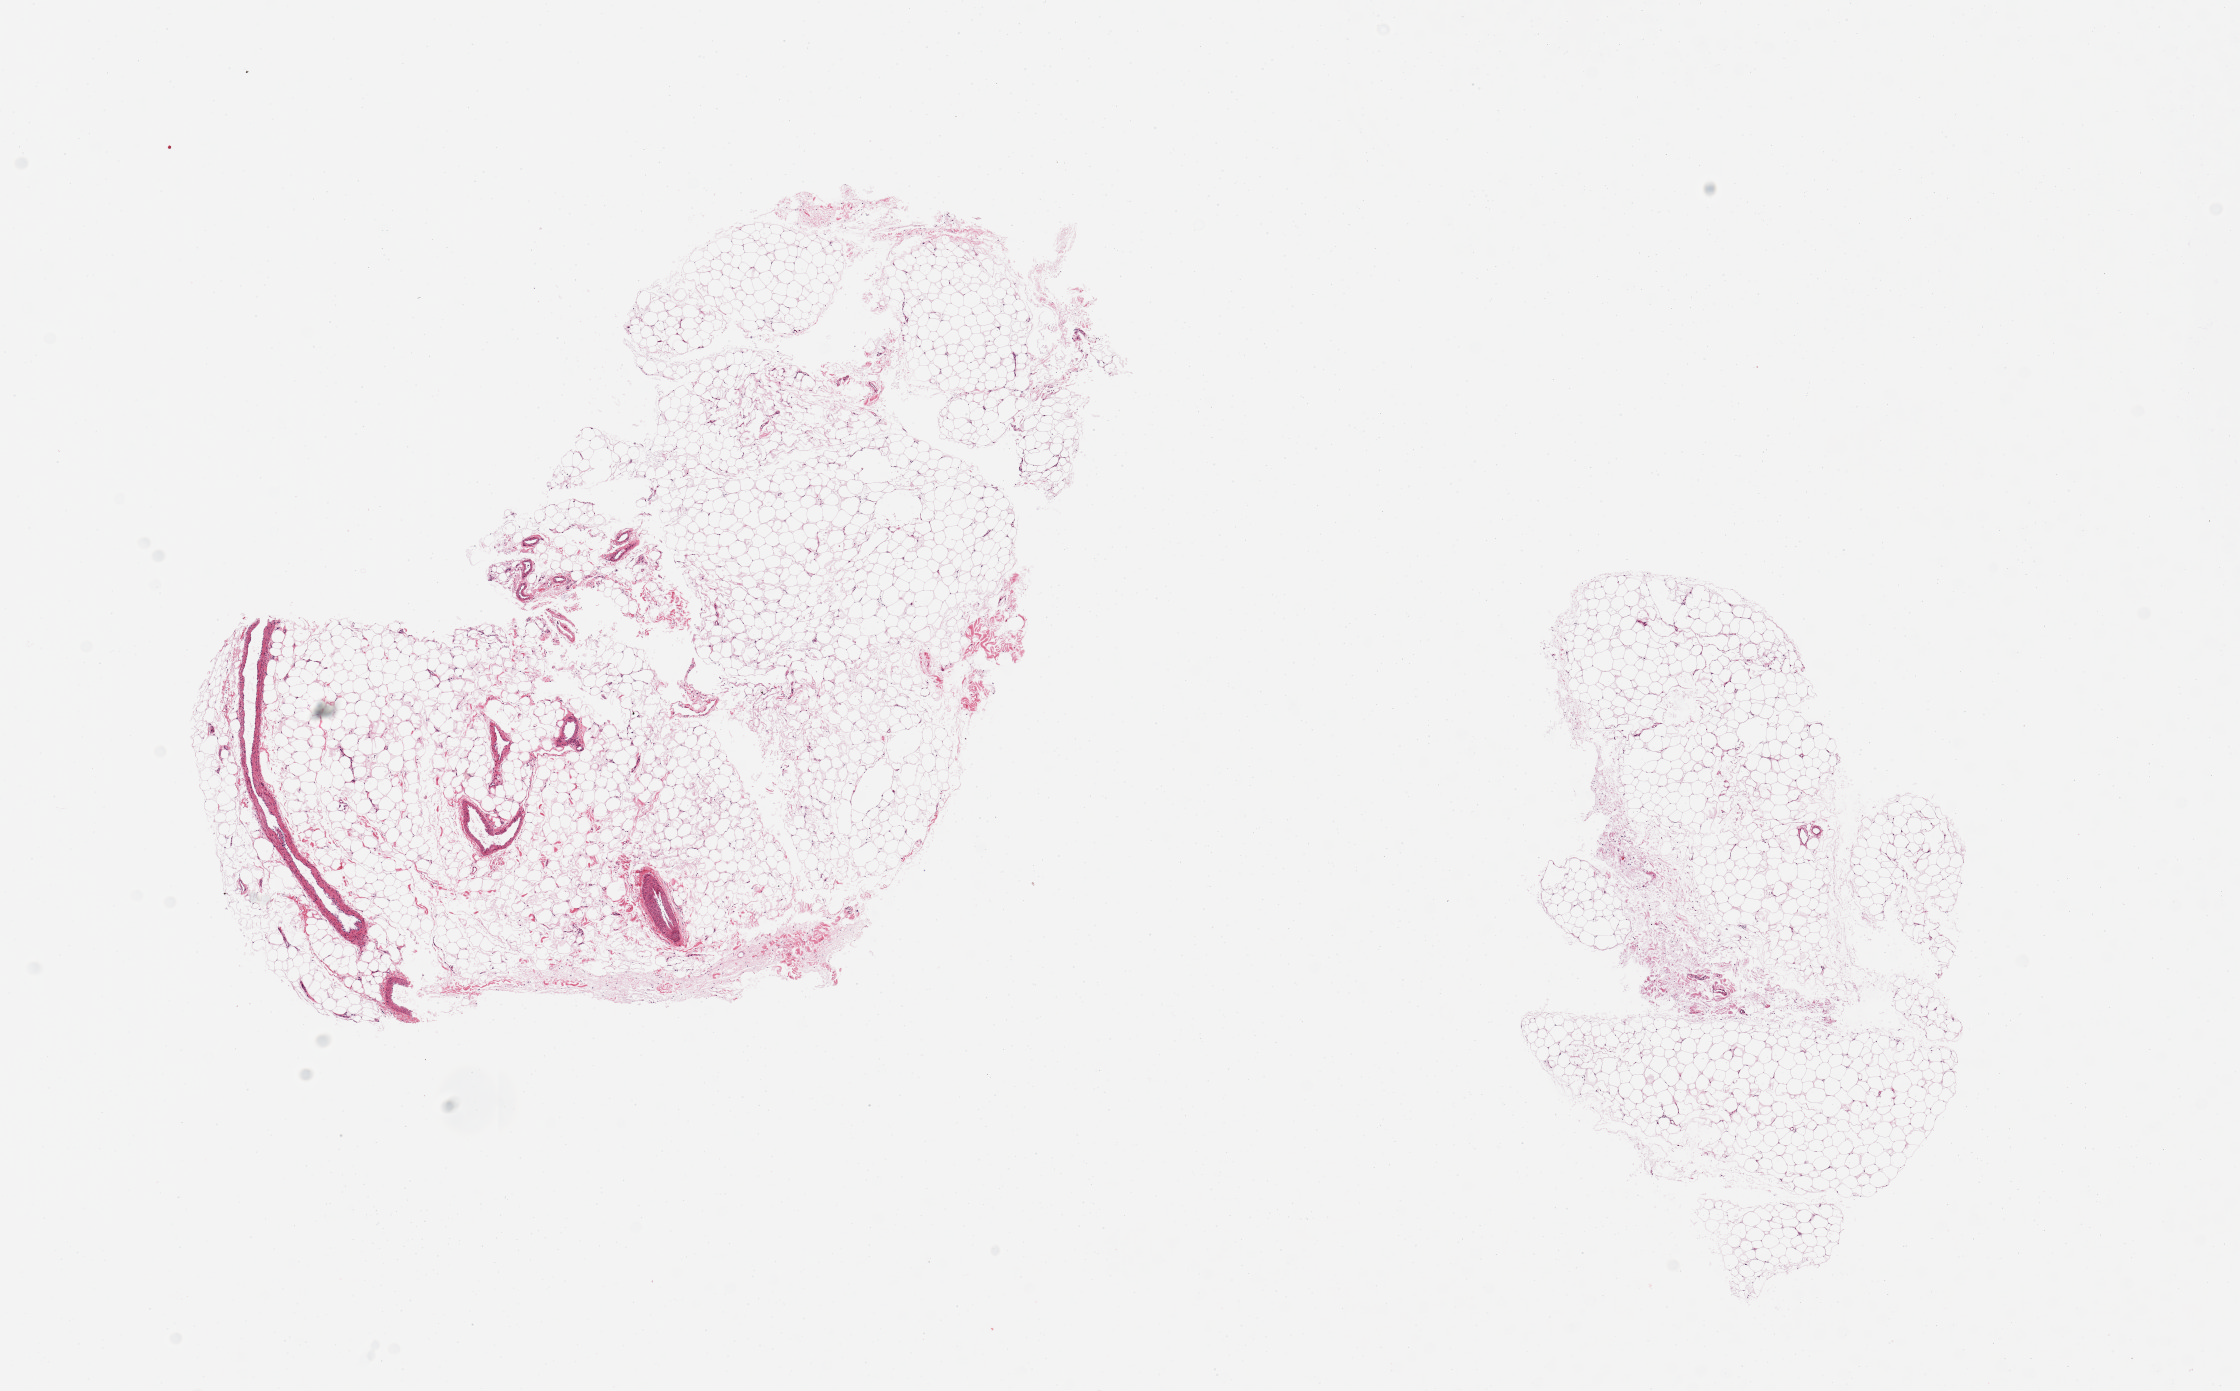
Whole-slide image, H&E stain — whole scanned area (about 17.7 x 11.0 mm) shown as a low-resolution overview. PAXgene-fixed paraffin-embedded (PFPE) section. Target tissue: transverse colon. Donor tissue sample. Donor sex: male.
Pathologist's review note for this sample: 2 pieces; fibroadipose tissue only; no evidence of colonic mucosa or muscularis.